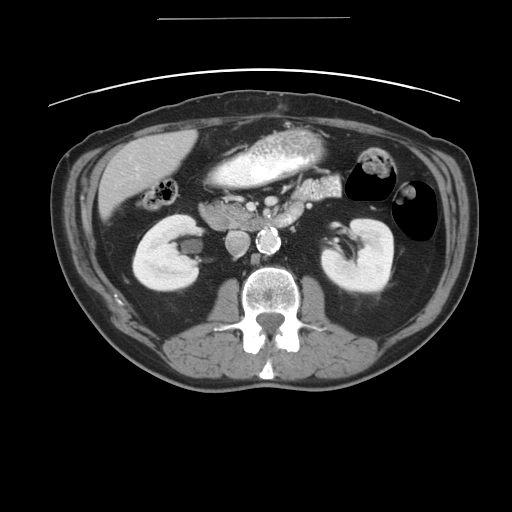
Contrast-enhanced abdominal CT, one axial slice; 120 kVp; soft-tissue window (W 400 / L 40 HU); 5 mm slice thickness; 512 × 512 image matrix, field of view 413 × 413 mm. Male patient, age 57 years. From the clinical record (not read from this slice): diagnosis: colorectal cancer liver metastases, imaged before liver resection; multiple liver metastases: yes; largest metastasis: 4 cm; disease in both lobes: no.
Structures marked on this image (outlined manually by an expert reader):
- liver: bounding box <98,130,196,218> (left, top, right, bottom; pixels)